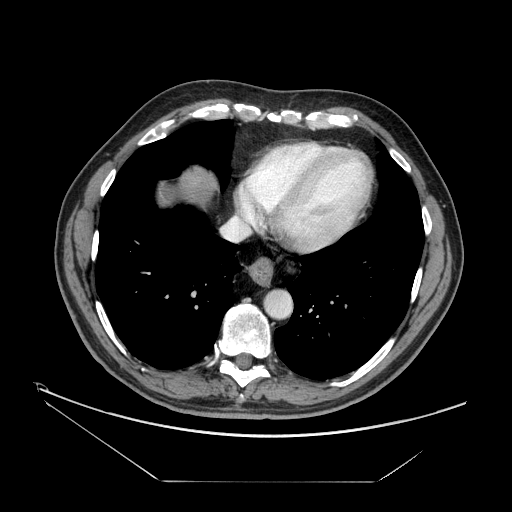
Contrast-enhanced abdominal CT, one axial slice. Position 154 of 161 along the scan axis. 120 kVp. Intravenous contrast given. Soft-tissue window (W 400 / L 40 HU). 2.5 mm slice thickness. 512 × 512 image matrix, field of view 440 × 440 mm. Male patient, age 65 years. Case-level facts recorded for this patient, not image findings: diagnosis: colorectal cancer liver metastases, imaged before liver resection; multiple liver metastases: yes; largest metastasis: 4.2 cm; disease in both lobes: yes.
Structures marked on this image (expert manual segmentation):
- hepatic veins: bounding box <221,162,267,242> (left, top, right, bottom; pixels)
- liver: <164,167,214,203>
- planned liver remnant (the part of the liver to remain after resection): <161,166,215,205>